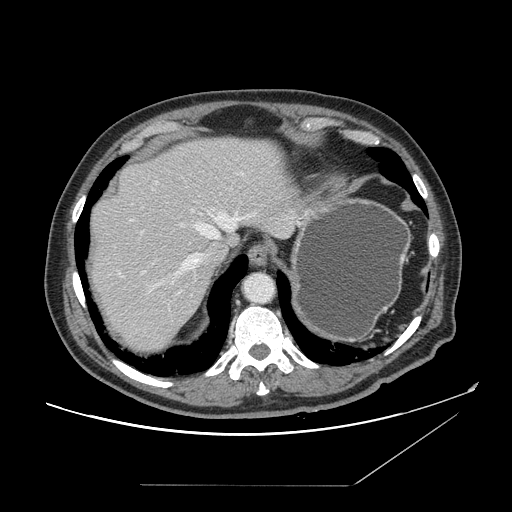
Contrast-enhanced abdominal CT, one axial slice. Position 127 of 166 along the scan axis. Soft-tissue window (W 400 / L 40 HU). 2.5 mm slice thickness. 512 × 512 image matrix, field of view 416 × 416 mm. Male patient, age 80 years. Case-level facts recorded for this patient, not image findings: diagnosis: colorectal cancer liver metastases, imaged before liver resection; multiple liver metastases: no; largest metastasis: 2.2 cm; disease in both lobes: no.
Structures marked on this image (expert manual segmentation):
- hepatic veins: bounding box [x1, y1, x2, y2] px = [153, 209, 253, 288]
- liver: [89, 138, 296, 352]
- planned liver remnant (the part of the liver to remain after resection): [90, 138, 296, 256]
- portal vein (with intrahepatic branches): [142, 210, 195, 233]